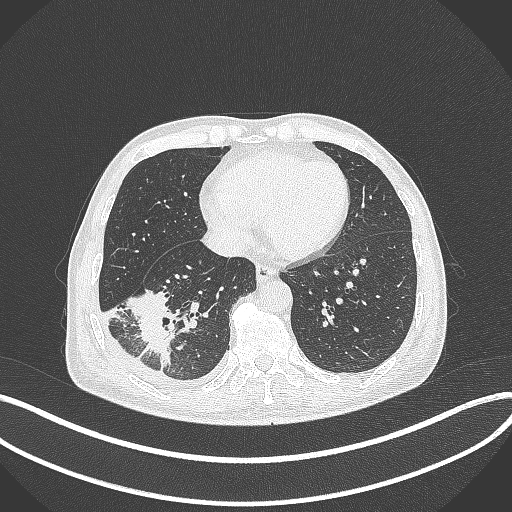
Chest CT, one axial slice. Position 123 of 388 along the scan axis. Reconstruction kernel B70f. 120 kVp. Lung window (W 1500 / L -600 HU). 1 mm slice thickness. 512 × 512 image matrix. Patient: male, 64 years. From the clinical record (not read from this slice): clinical TNM (as recorded): T3 N0 M0.
Structures marked on this image (rectangle marked by the reading radiologist):
- lung tumour (recorded histology: adenocarcinoma): bounding box [x1, y1, x2, y2] px = [126, 282, 180, 378]